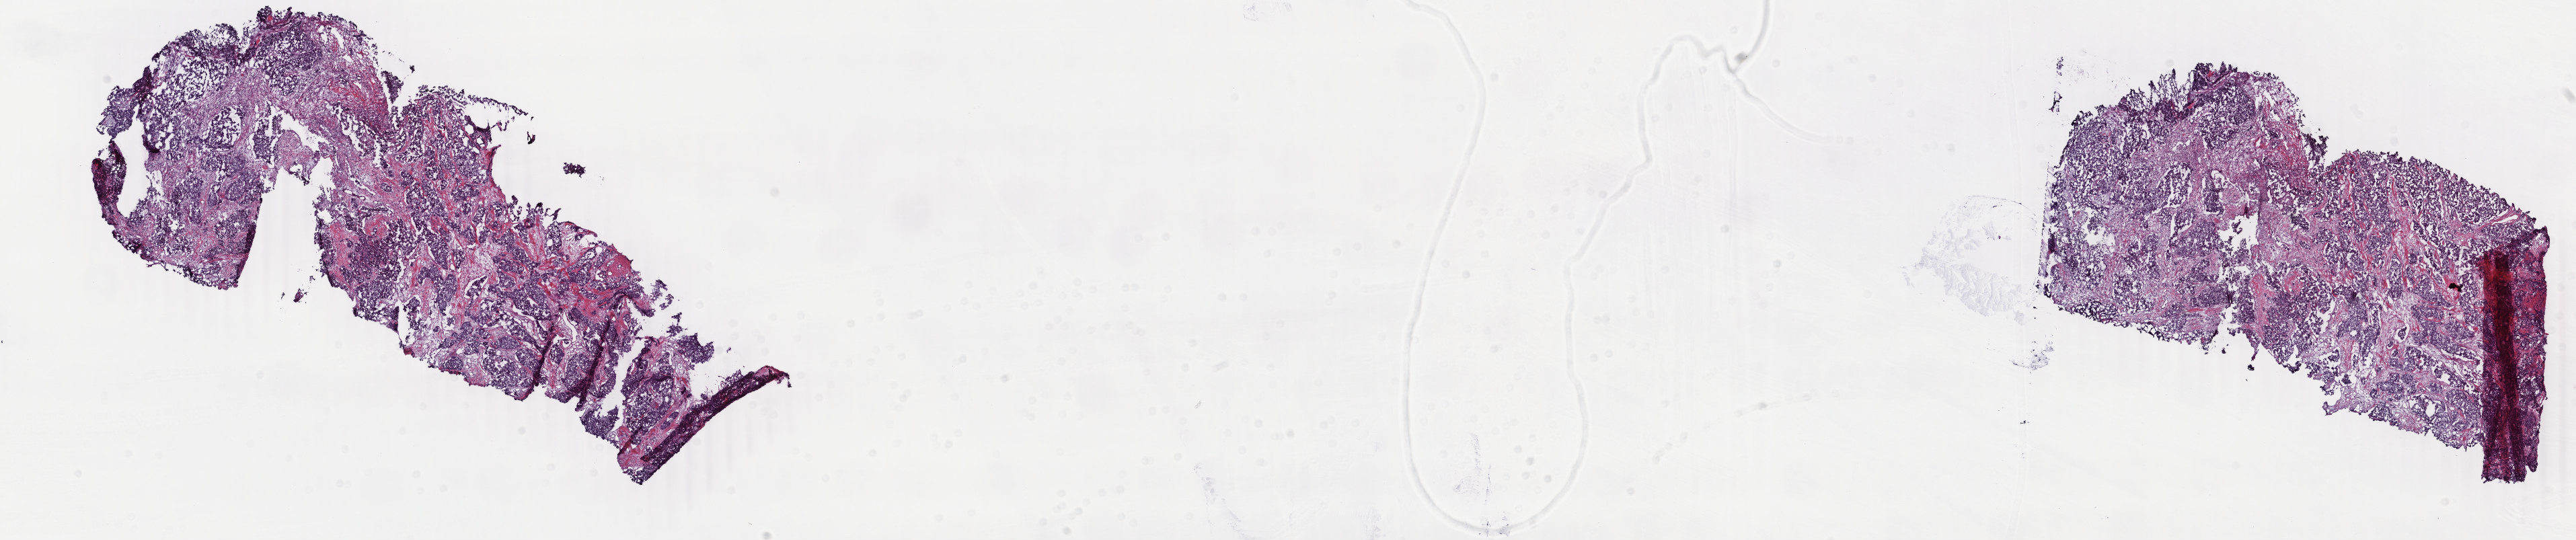
Hematoxylin and eosin (H&E) stained whole-slide image — a low-resolution overview of the entire scanned area, about 30.5 x 6.4 mm (from a 40x scan); frozen section from the top of the tissue portion; primary tumour sample from the breast. Female, age 54 years at initial diagnosis. Composition of this section per pathologist review: tumour cells 75%, tumour nuclei 85%, normal cells 0%, stromal cells 23%, necrosis 2%. Infiltration values recorded for this section: lymphocyte infiltration 7%, monocyte infiltration 3%, neutrophil infiltration 1%.
• AJCC pathologic stage: IIB
• TNM: T2 N1 M0
• pathologic diagnosis: Infiltrating duct carcinoma, NOS
• laterality: right